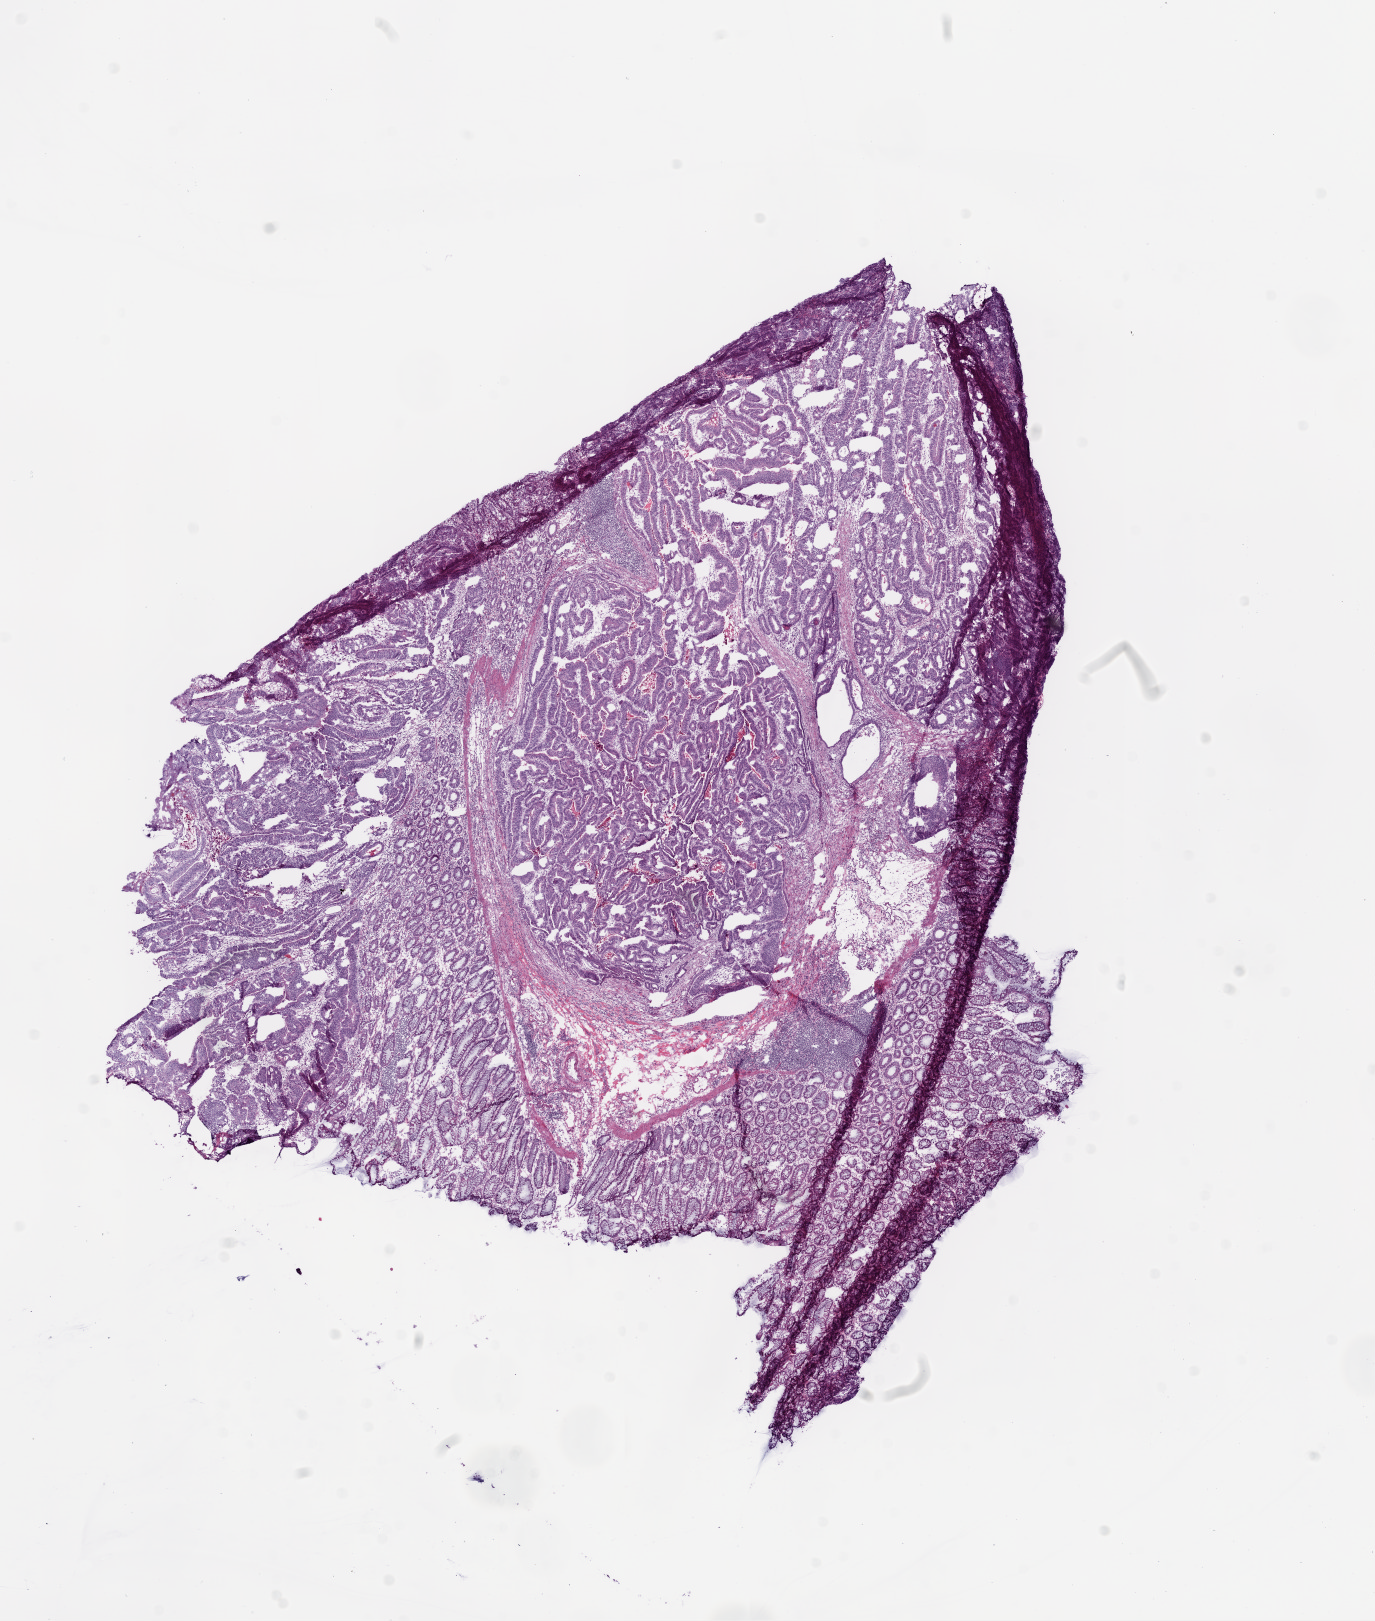
Hematoxylin and eosin (H&E) stained whole-slide image — low-resolution overview of the scanned area, about 11.0 x 13.0 mm (slide scanned at 20x); frozen section from the bottom of the tissue portion; sample: primary tumour, colon. Male, age 77 years at initial diagnosis. Pathologist review of this section (percent, as recorded): tumour cells 65%, tumour nuclei 65%, normal cells 15%, stromal cells 10%, necrosis 10%.
AJCC pathologic stage: I (5th edition). Lymph nodes positive (case pathology): 0 of 46 examined. Histologic diagnosis: Adenocarcinoma, NOS.